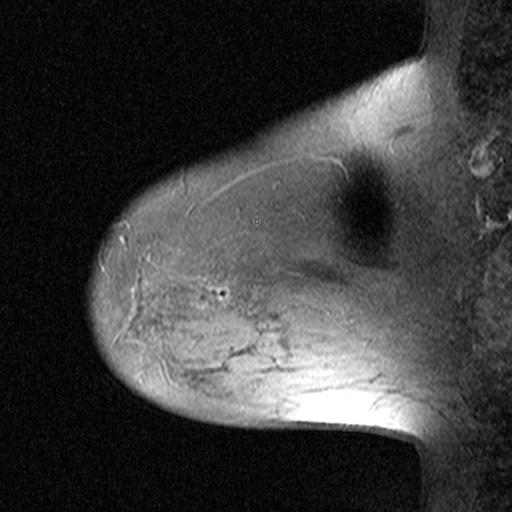
Breast MRI (dynamic contrast-enhanced), one sagittal slice; slice 35 of 44 in the series (ordered by position); dynamic contrast-enhanced study with each time point stored as its own series, time point 2 of 3 at this slice position (early post-contrast, ordered by acquisition time); 1.5 T; TE 4.5 ms, TR 11 ms; 3 mm slice thickness; 512 × 512 image matrix. Patient: female, 38 years. From the clinical record (not read from this slice): setting: breast cancer imaged before/during neoadjuvant chemotherapy; receptor status: HR-positive, HER2-negative.
Annotated regions visible in this slice (semi-automatically segmented with operator editing):
- analysis volume of interest (the breast-tissue region the enhancement analysis was run in; not a lesion): bounding box <152,236,253,335> (left, top, right, bottom; pixels)
- tumour enhancement mask (voxels above the 90 % enhancement threshold inside the analysis volume of interest): <212,286,227,300>